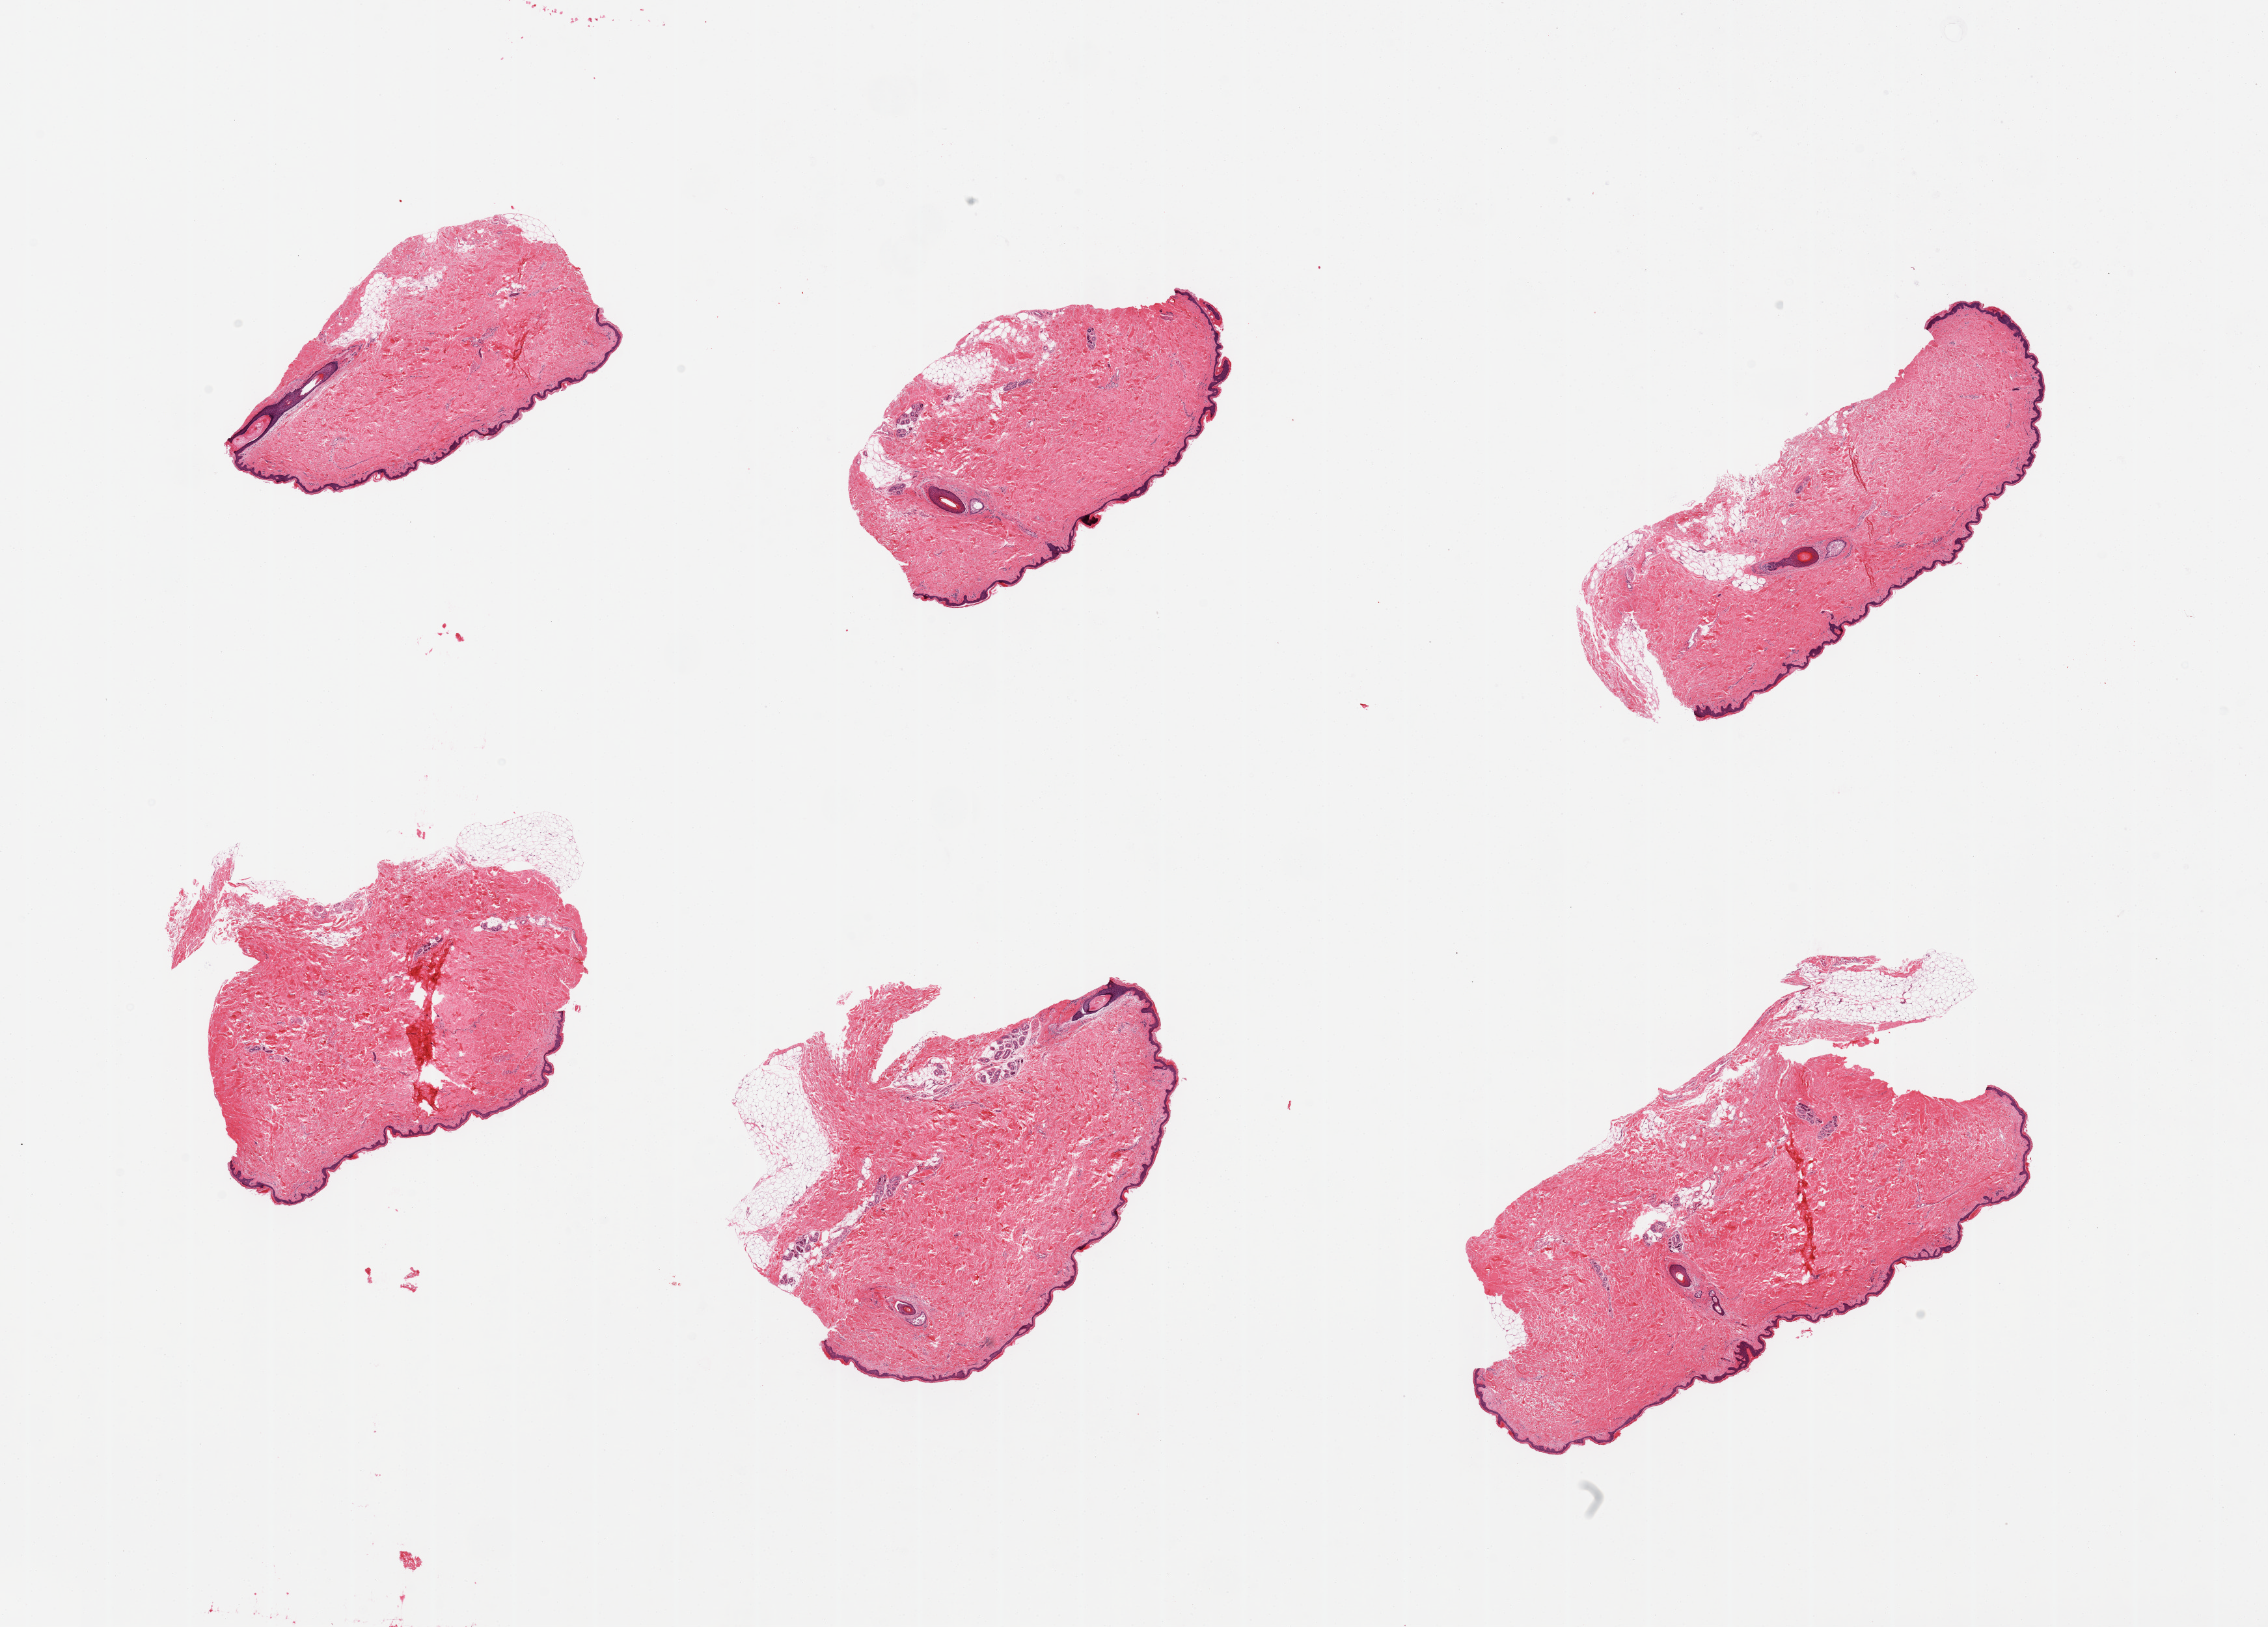
Whole-slide image, H&E stain, brightfield, whole scanned area (about 27.6 x 19.8 mm) shown as a low-resolution overview, PAXgene-fixed, paraffin-embedded tissue, sampled site (target tissue): skin of suprapubic region, tissue donor sample.
Reviewer comment on this tissue sample: 6 pieces, minimal dermal fat; squamous epithelium is ~60-70 microns.